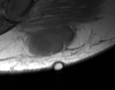
MRI of an extremity soft-tissue mass, one axial slice. Slice 14 of 35 in the series (ordered by position). MR volume resampled by the dataset authors to the PET/CT grid (not the native acquisition matrix). 3.27 mm slice thickness. 115 × 90 image matrix, field of view 112 × 88 mm. Male patient. Case-level facts recorded for this patient, not image findings: histological type: pleiomorphic leiomyosarcoma; grade: high; site of the primary tumour: left buttock.
Annotated regions visible in this slice (expert contour drawn on MRI and transferred to this co-registered scan by the dataset authors):
- gross tumour volume including surrounding oedema: bounding box [x1, y1, x2, y2] px = [26, 23, 79, 56]
- gross tumour volume (mass): [30, 25, 77, 56]